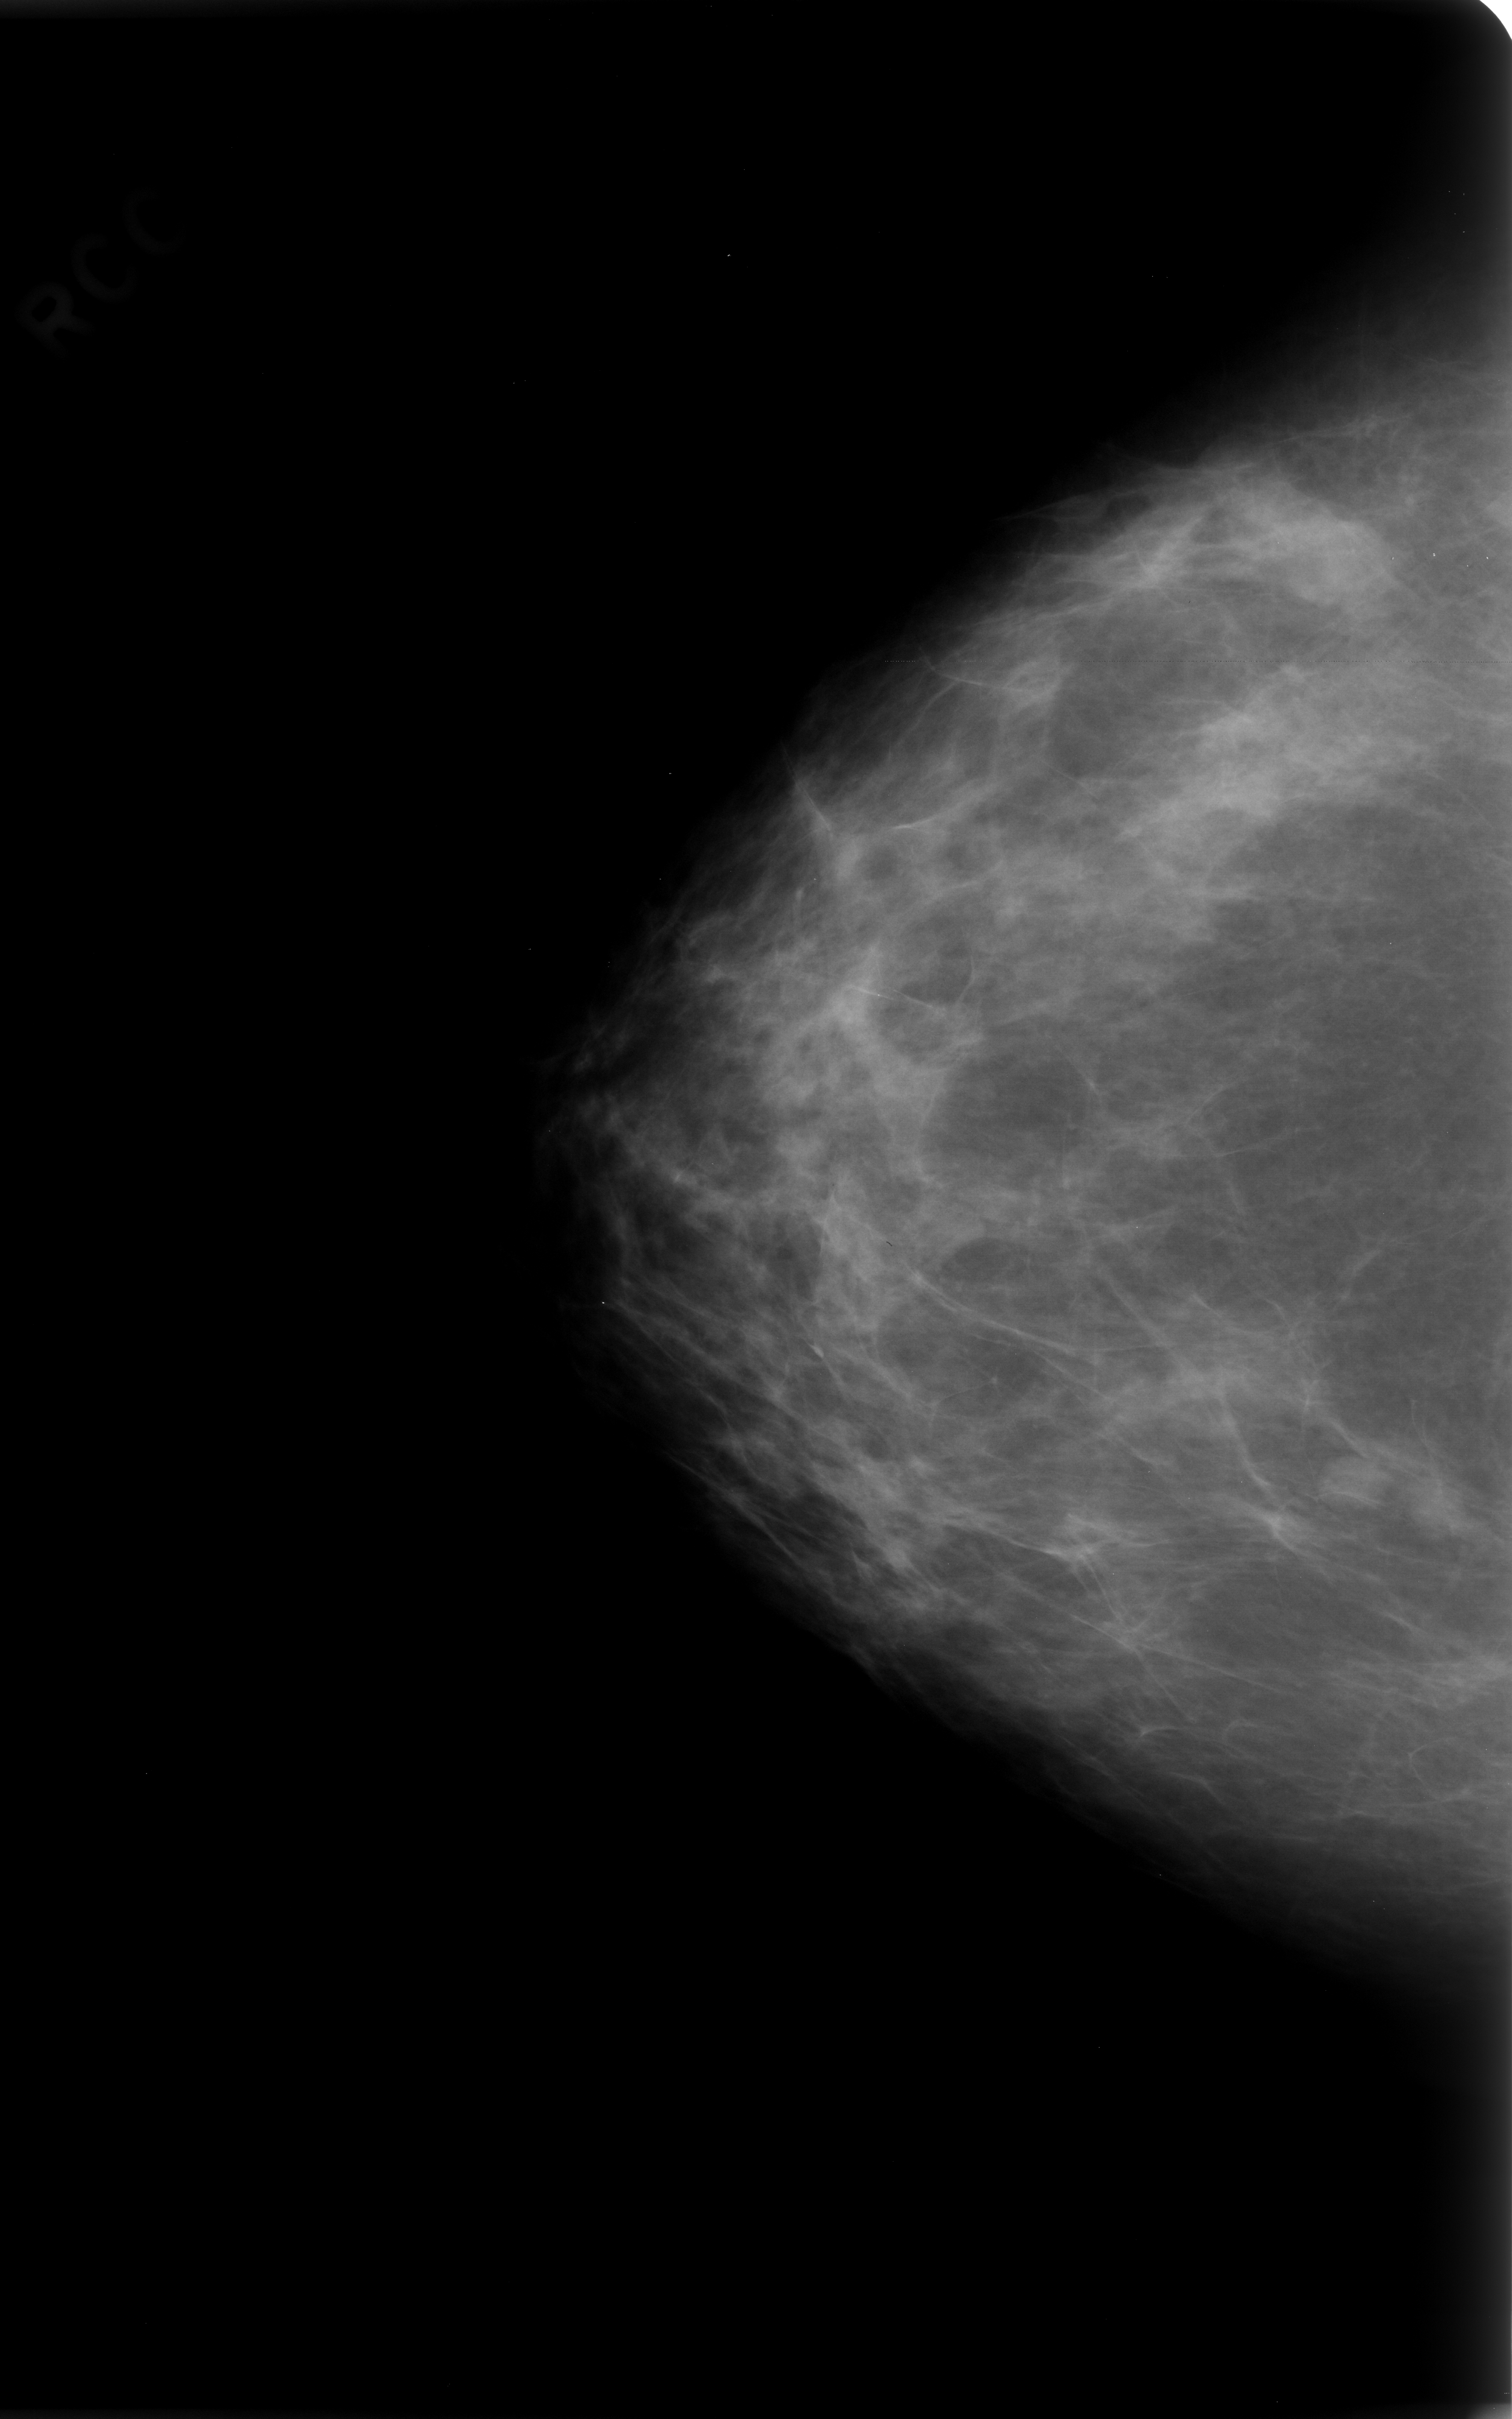
Digitized screen-film mammogram. Right breast. CC view. 1512 × 2419 image matrix.
Marked abnormalities (boxes around the expert regions of interest):
- Finding 1 of 3: mass, shape lobulated, margins circumscribed; BI-RADS assessment category 3; pathology (as recorded): benign: box from (x=1265, y=498) to (x=1402, y=630) px
- Finding 2 of 3: mass, shape oval, margins circumscribed; BI-RADS assessment category 3; pathology result (as recorded, not read from the image): benign: (x=1306, y=1422)–(x=1399, y=1511)
- Finding 3 of 3: mass, shape round, margins circumscribed; BI-RADS assessment category 3; subtlety rating 5 on a 1 (subtle) to 5 (obvious) scale; pathology result (as recorded, not read from the image): benign: (x=1402, y=1445)–(x=1481, y=1542)